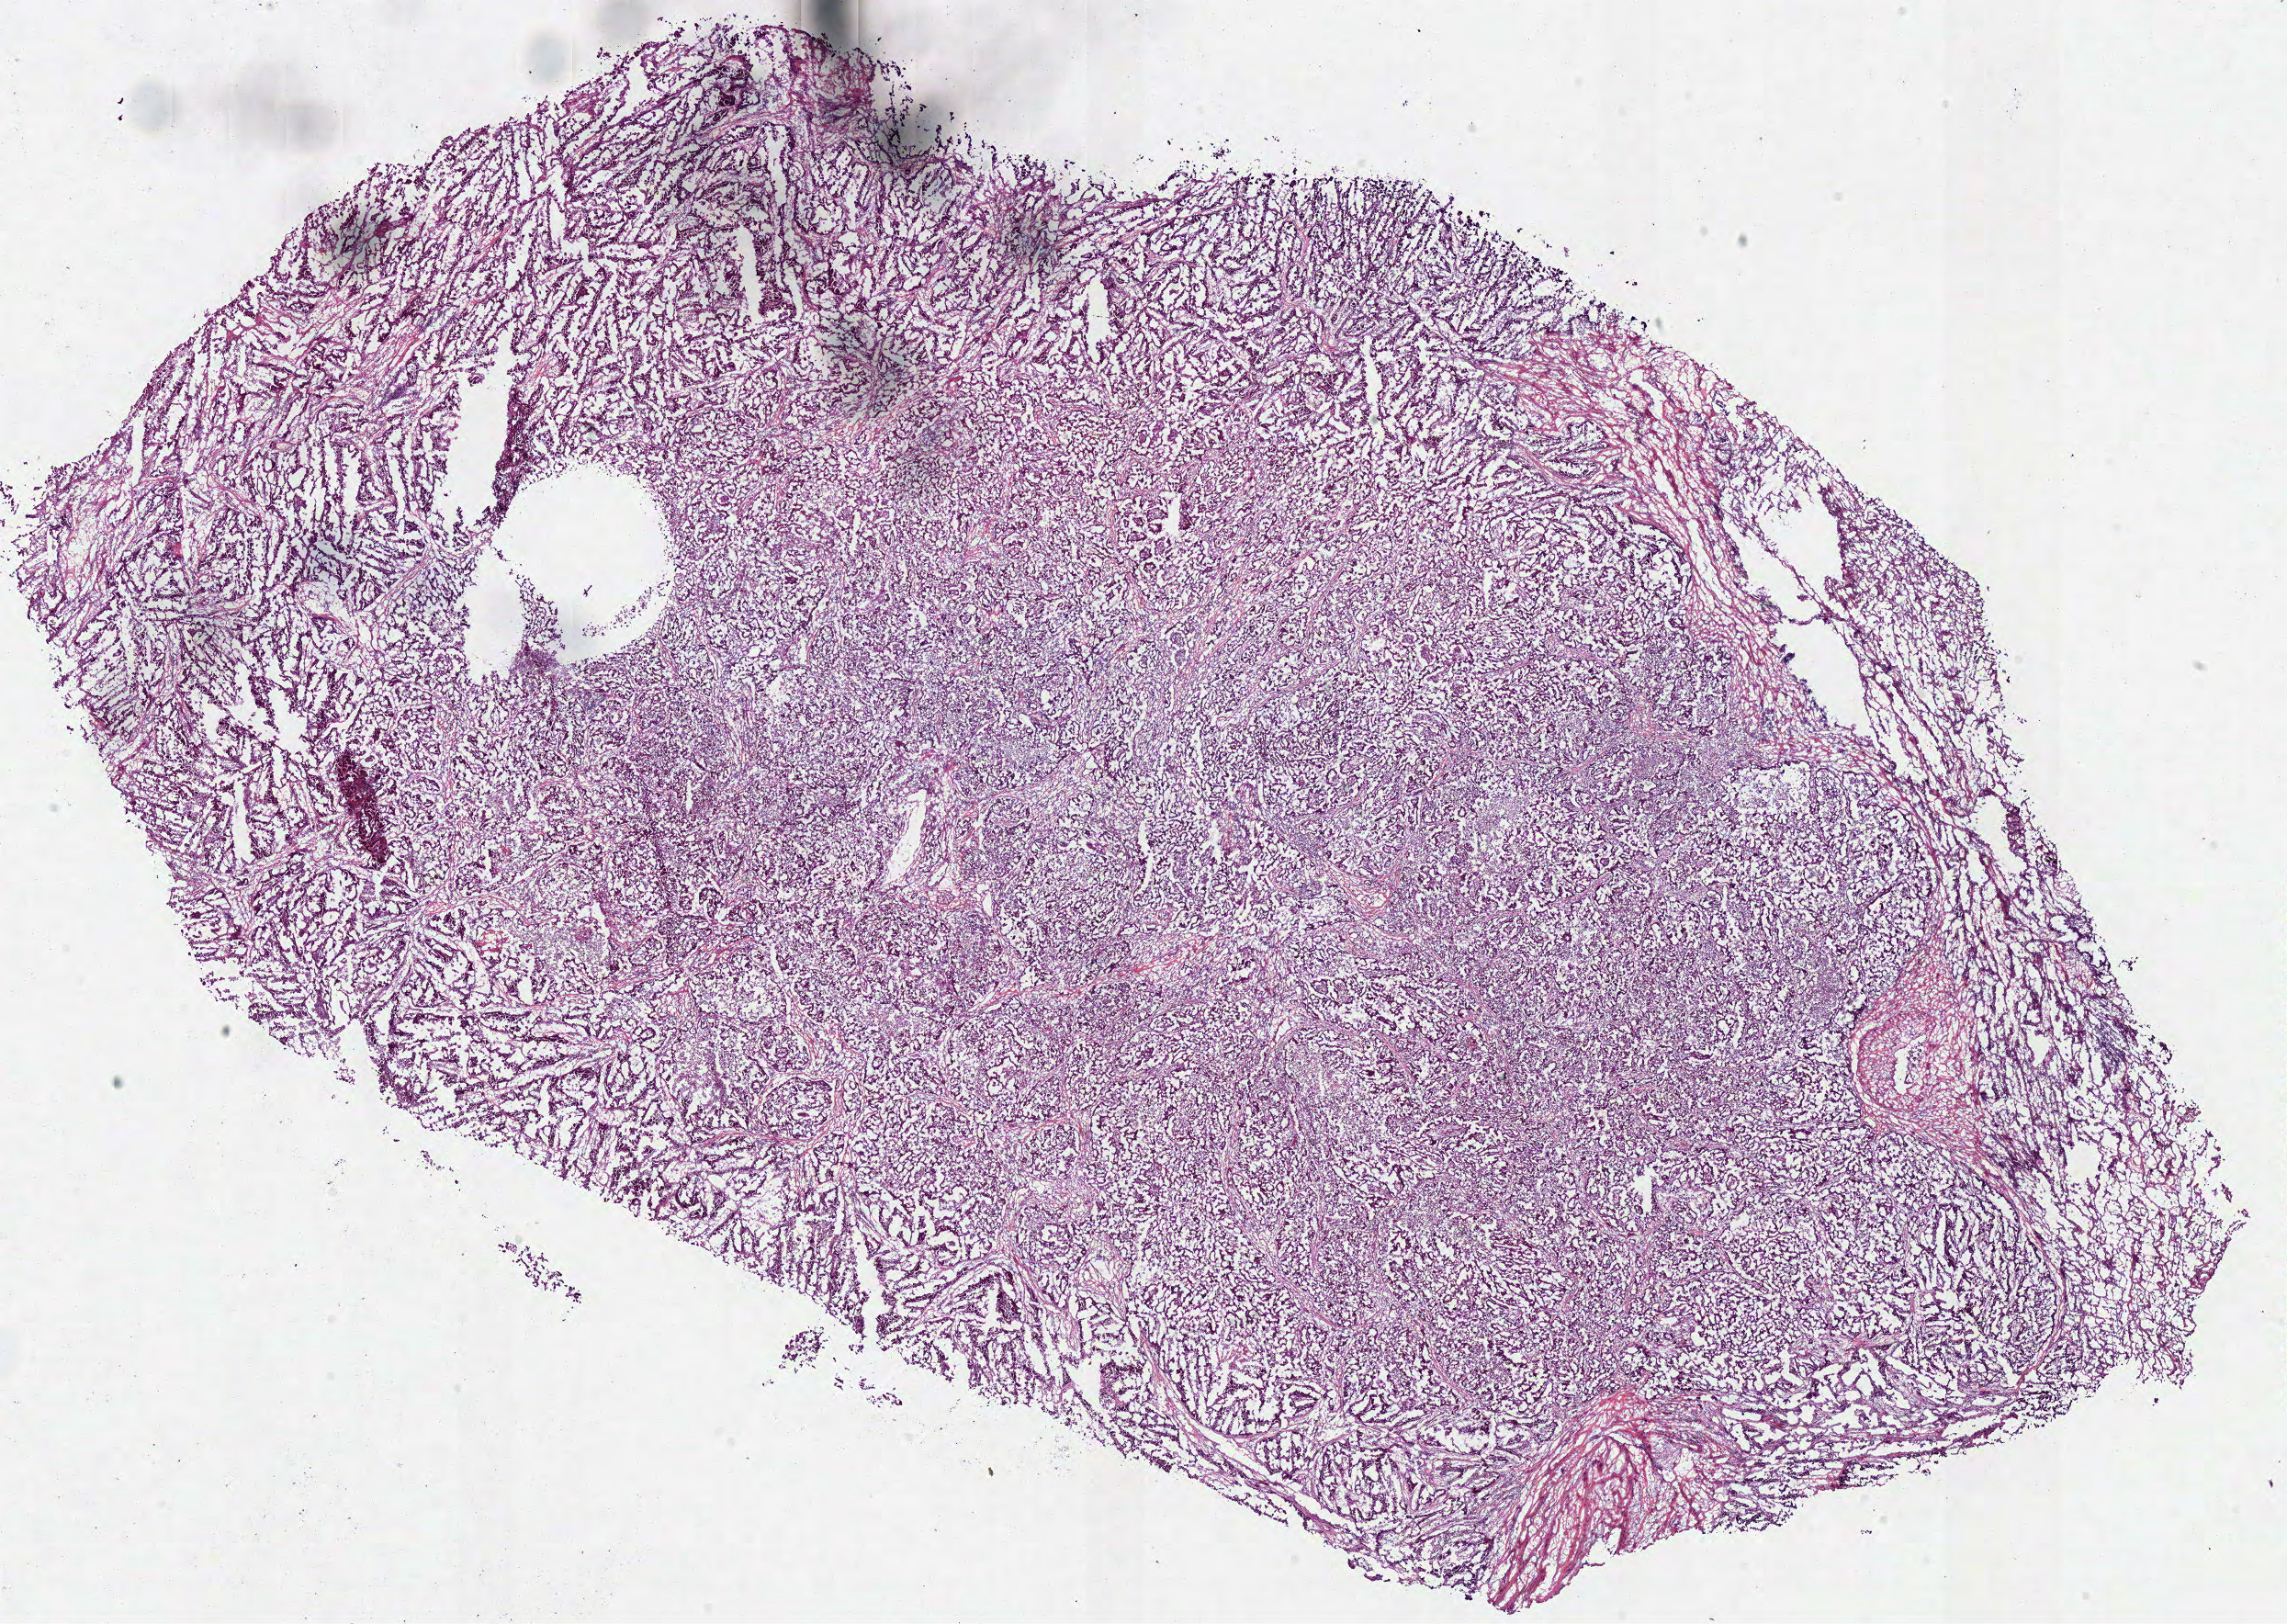
H&E-stained whole-slide image, low-resolution overview of the scanned area, about 19.6 x 13.9 mm. Frozen section from the bottom of the tissue portion. Primary tumour sample from the lung. Female, age 48 years at initial diagnosis. Composition of this section per pathologist review: tumour cells 85%, tumour nuclei 80%, normal cells 5%, stromal cells 10%, necrosis 0%.
* histologic diagnosis: Papillary adenocarcinoma, NOS (upper lobe, lung)
* laterality: right
* AJCC pathologic stage: IB (6th edition)